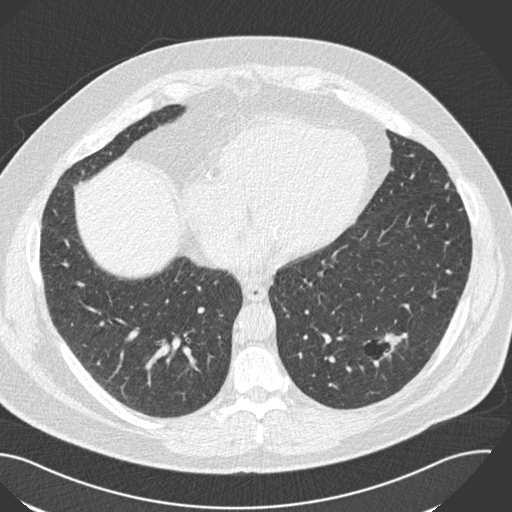
Chest CT (low-dose screening protocol), one axial image; third annual screen; lung window (W 1500 / L -600 HU); standard (soft-tissue) reconstruction kernel (B30f); 120 kVp; slice 89 of 153 in the series. Male participant, aged 57 years at enrolment. Current smoker at enrolment.
Expert-annotated lung lesion, bounding box [x1, y1, x2, y2] px = [349, 318, 424, 379]. Screening reader's record for this exam (one nodule recorded; not confirmed to be the boxed lesion): non-calcified nodule or mass ≥4 mm, left lower lobe, 22 × 18 mm, poorly defined margins, soft tissue attenuation, pre-existing on the prior screen: yes; interval growth: yes. Lung cancer was diagnosed 124 days after this screen: squamous cell carcinoma, NOS, left lower lobe, moderately differentiated (G2), stage IA (AJCC 6th edition), 22 mm at pathology.